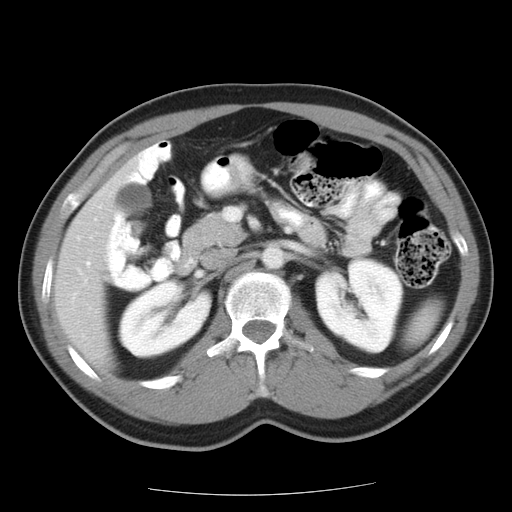
Contrast-enhanced abdominal CT, one axial slice; position 6 of 22 along the scan axis; reconstruction kernel STANDARD; intravenous contrast given; soft-tissue window (W 400 / L 40 HU); 512 × 512 image matrix, field of view 359 × 359 mm. Male patient, age 41 years. From the clinical record (not read from this slice): diagnosis: colorectal cancer liver metastases, imaged before liver resection; multiple liver metastases: no; largest metastasis: 2.7 cm.
Annotated regions visible in this slice (outlined manually by an expert reader):
- hepatic veins: box from (x=87, y=263) to (x=91, y=266) px
- liver: (x=56, y=175)–(x=124, y=358)
- planned liver remnant (the part of the liver to remain after resection): (x=56, y=173)–(x=124, y=358)